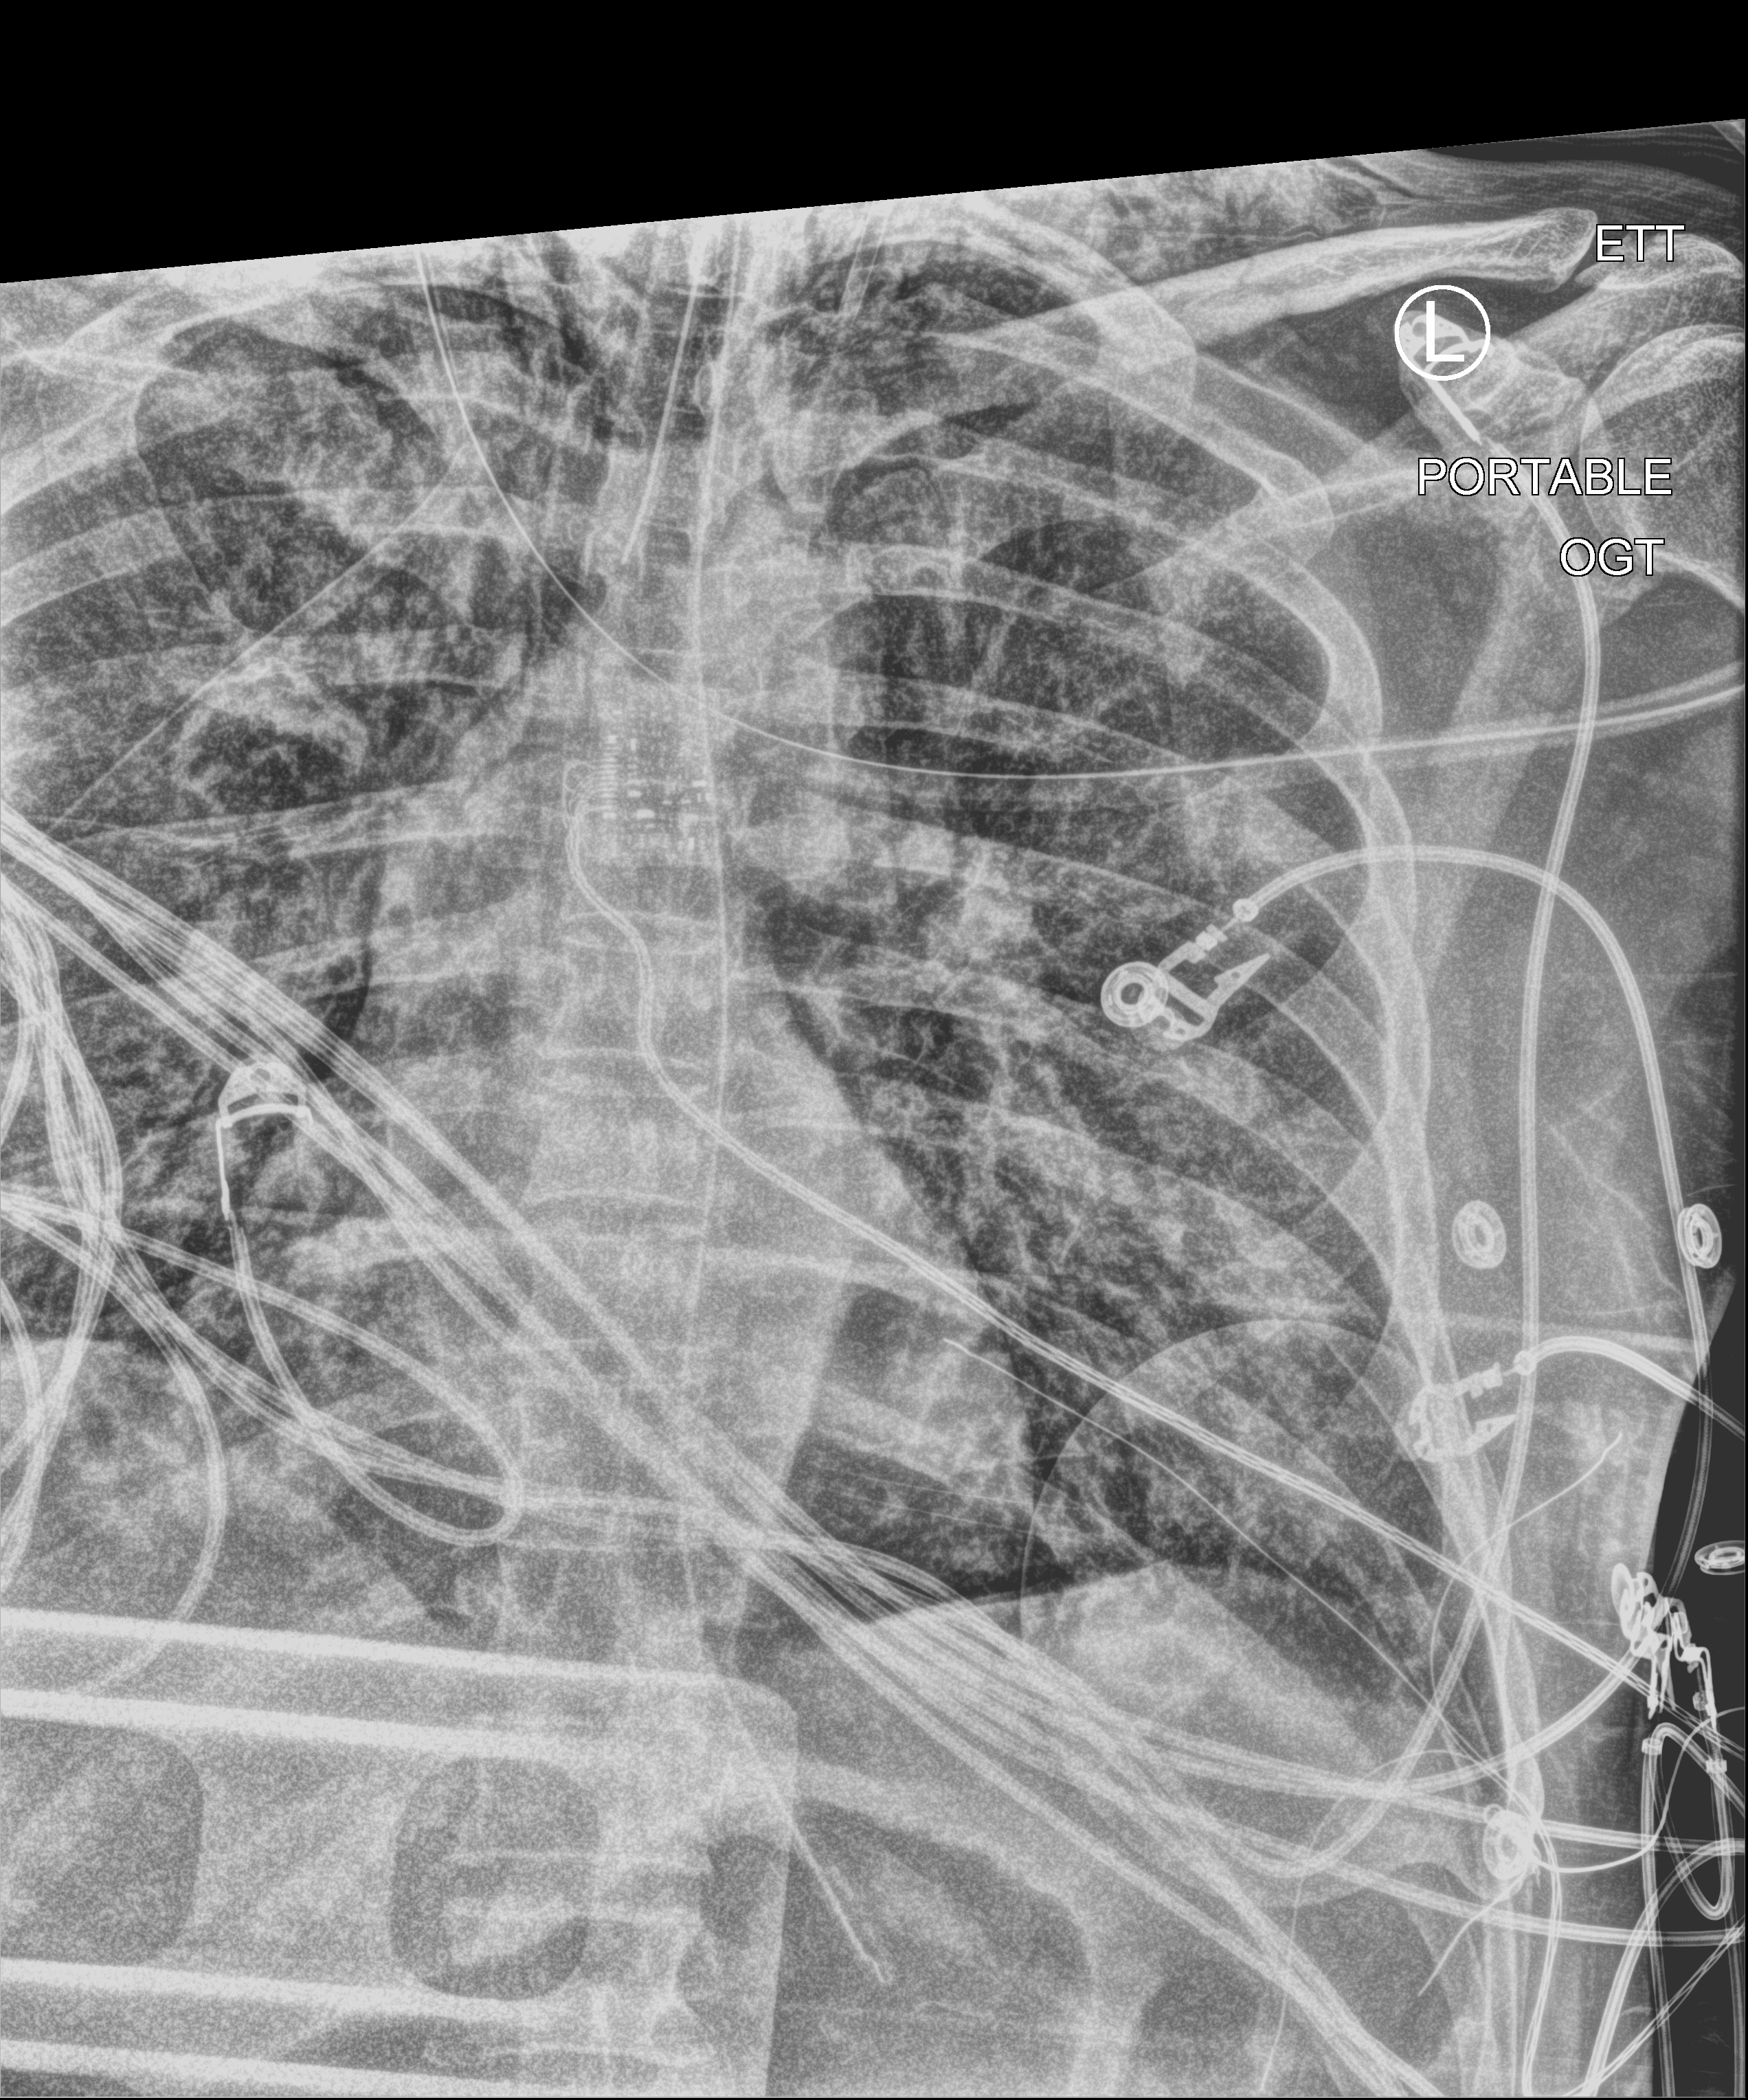
Chest X-ray (portable); anteroposterior (AP) projection. Patient hospitalised with COVID-19; male, aged 60–74 years.
Admission-level facts for this patient (not findings on this image; timing relative to this image not recorded):
- mechanically ventilated during this hospital stay: yes